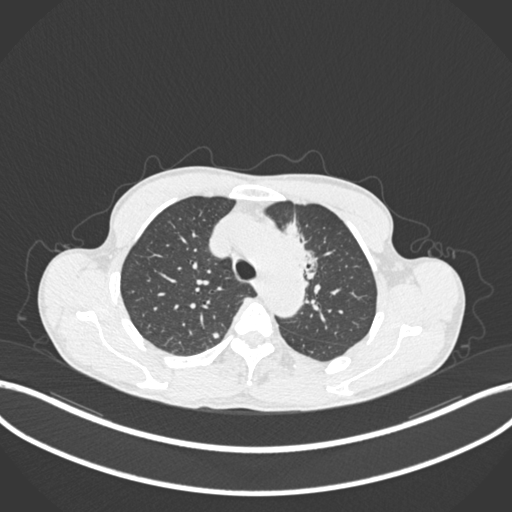
Chest CT, one axial slice. Slice 151 of 211 in the series (ordered by position). 120 kVp. Lung window (W 1500 / L -600 HU). 512 × 512 image matrix, field of view 400 × 400 mm. Male patient, age 58 years. From the clinical record (not read from this slice): clinical TNM (as recorded): T1c N1 M0.
Structures marked on this image (bounding box drawn by a radiologist):
- lung tumour (recorded histology: adenocarcinoma): bounding box [x1, y1, x2, y2] px = [279, 220, 321, 286]